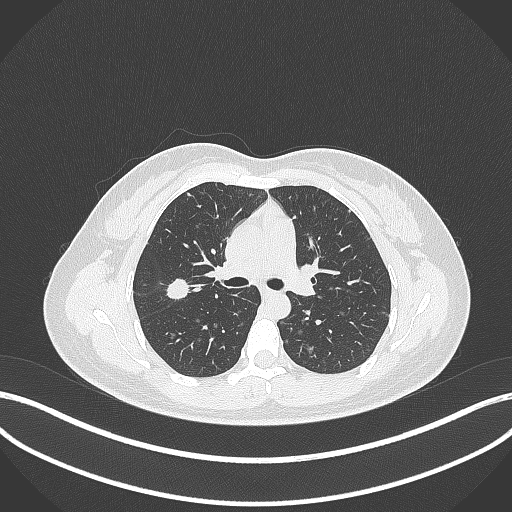
Chest CT, one axial slice. Position 210 of 307 along the scan axis. Reconstruction kernel B70f. 120 kVp. Lung window (W 1500 / L -600 HU). 1 mm slice thickness. 512 × 512 image matrix, field of view 400 × 400 mm. Patient: female, 33 years. From the clinical record (not read from this slice): clinical TNM (as recorded): T1c N0 M0; histopathological grade: G2-G3.
Structures marked on this image (bounding box drawn by a radiologist):
- lung tumour (recorded histology: adenocarcinoma): bounding box <164,277,191,301> (left, top, right, bottom; pixels)